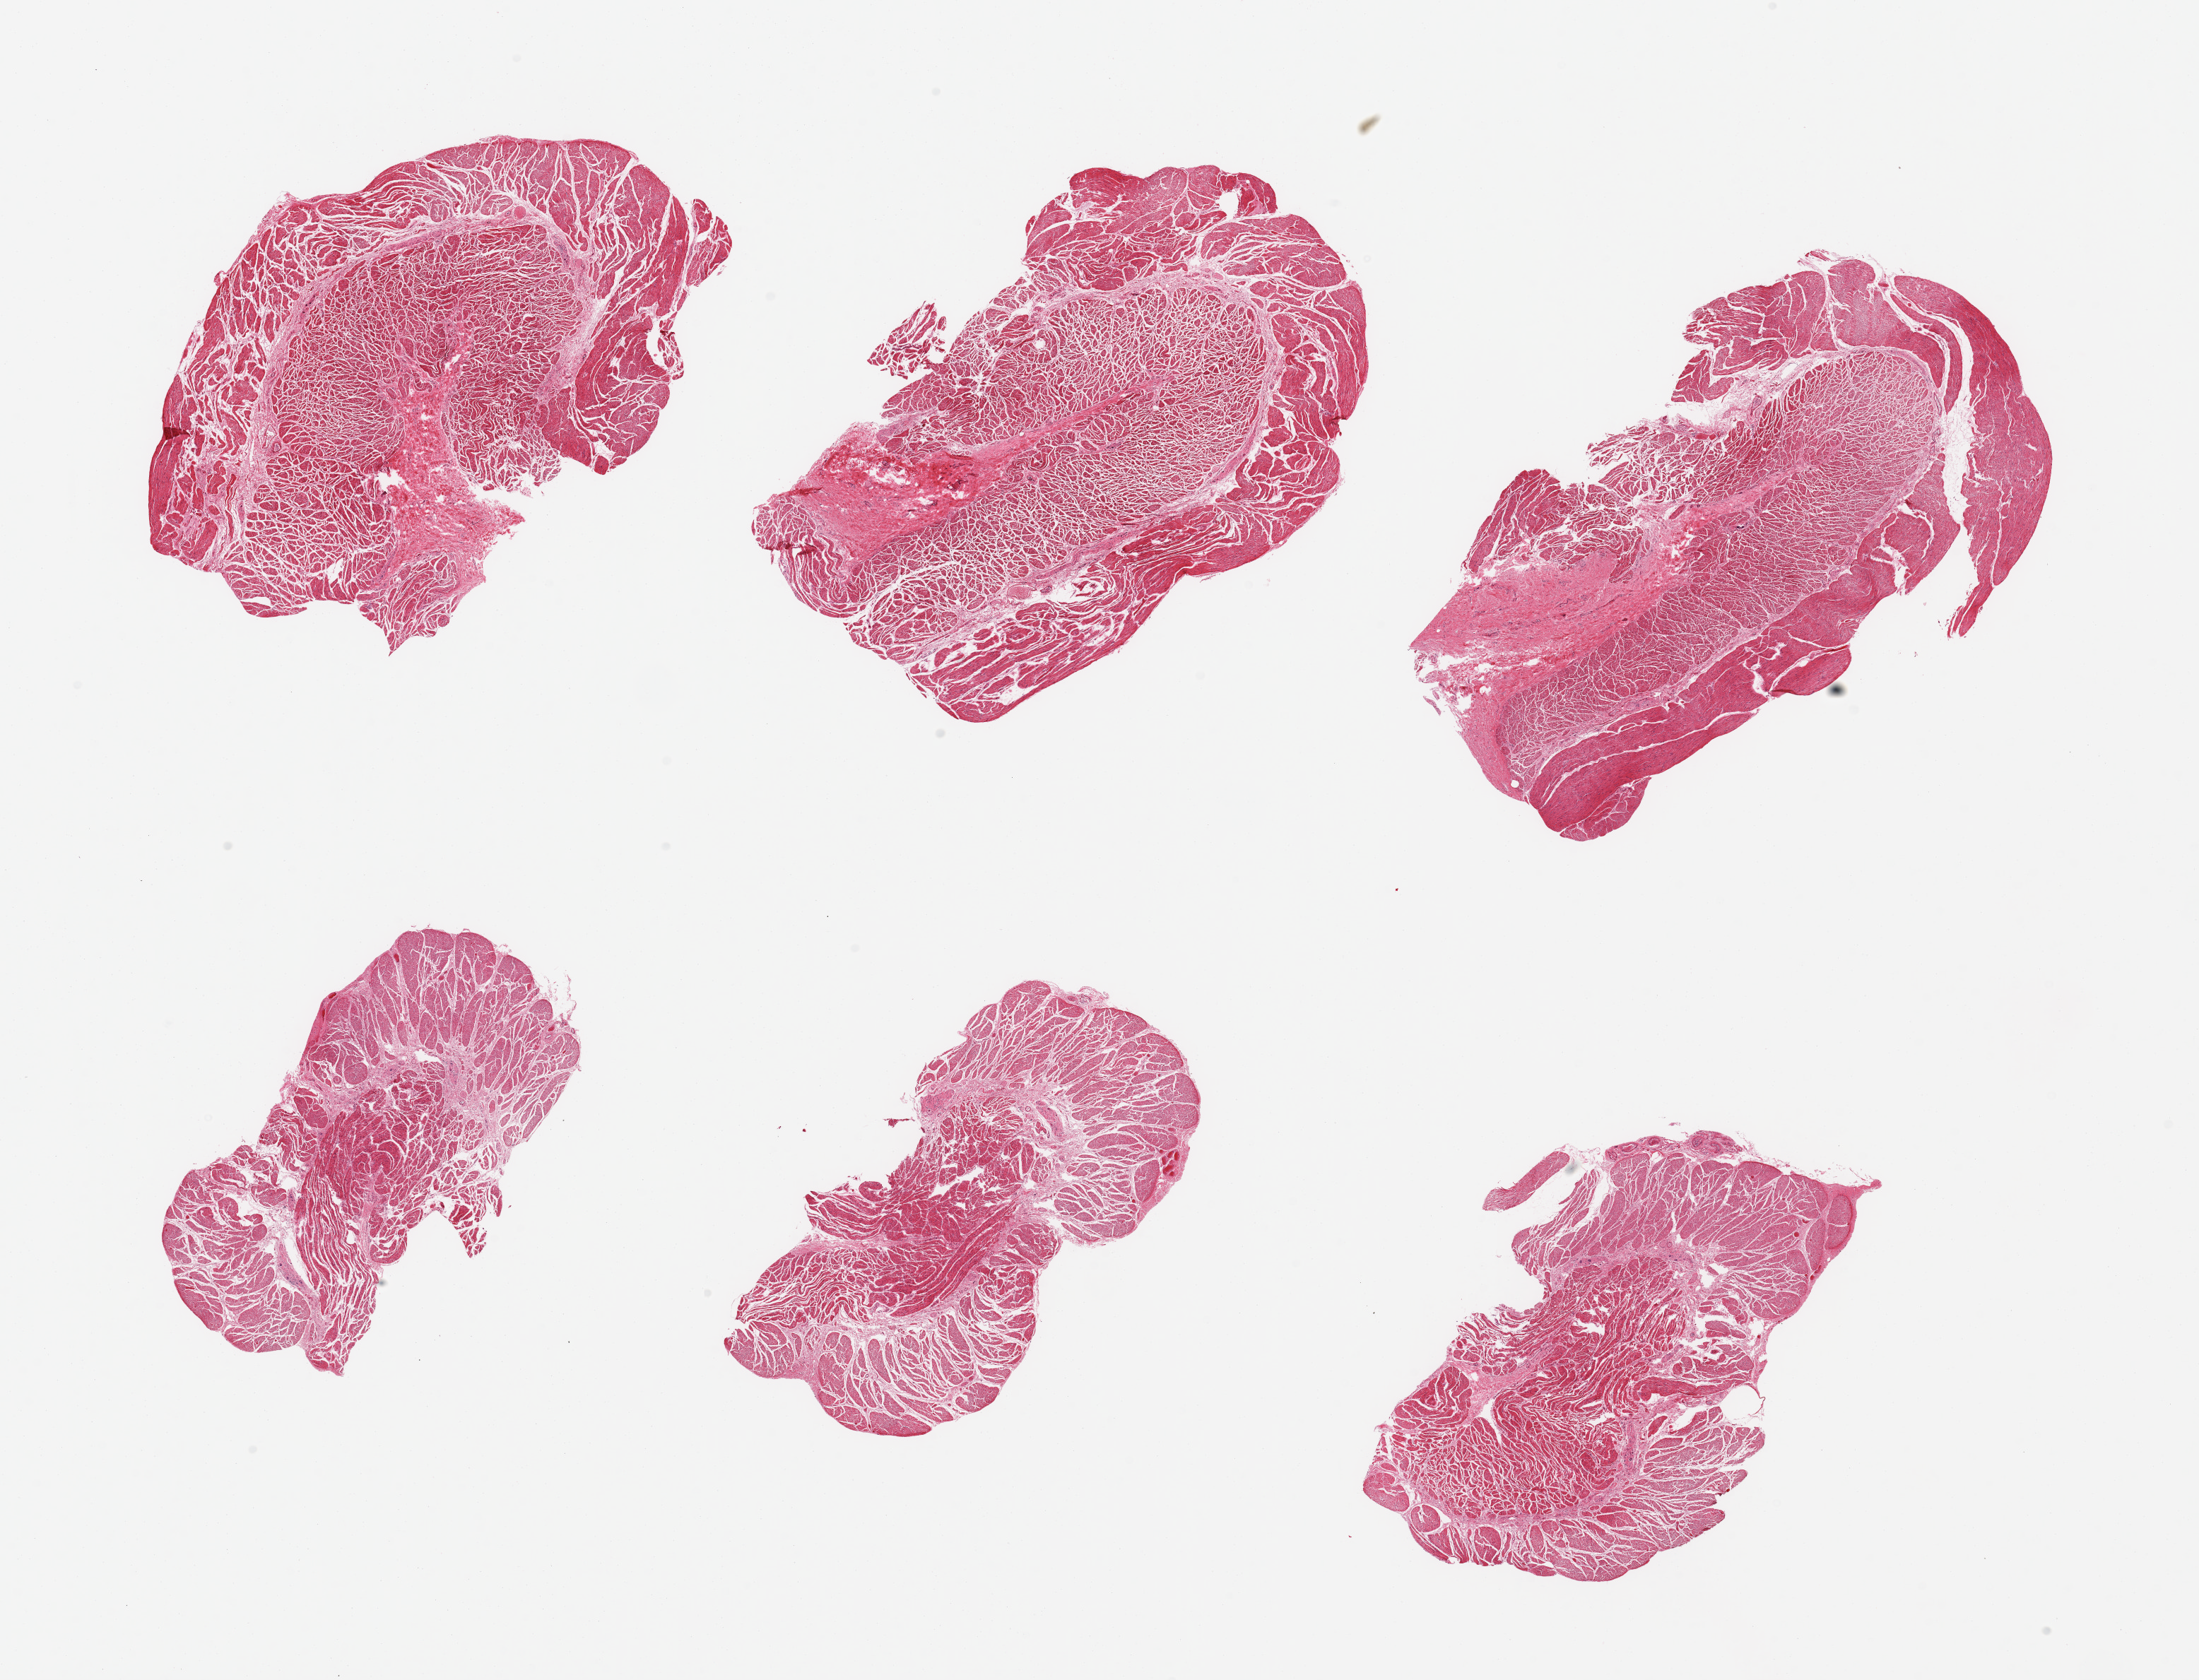
Haematoxylin and eosin whole-slide image, whole scanned area (about 24.6 x 18.8 mm, slide scanned at 20x) shown as a low-resolution overview; PAXgene-fixed, paraffin-embedded tissue; target tissue: esophageal muscle; tissue donor sample. Donor sex: male.
- review note (as recorded): 6 pieces; well dissected muscularis